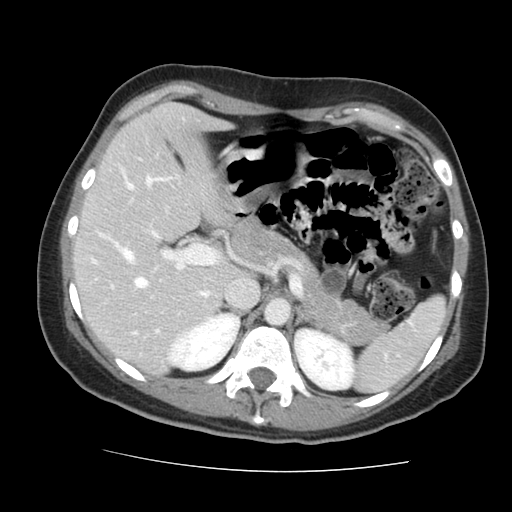
Contrast-enhanced abdominal CT, one axial slice. Position 94 of 144 along the scan axis. 120 kVp. Intravenous contrast given. Soft-tissue window (W 400 / L 40 HU). 512 × 512 image matrix. Female patient, age 46 years. From the clinical record (not read from this slice): diagnosis: colorectal cancer liver metastases, imaged before liver resection; multiple liver metastases: no; largest metastasis: 2.8 cm; disease in both lobes: no.
Structures marked on this image (expert manual segmentation):
- hepatic veins: bounding box [x1, y1, x2, y2] px = [122, 171, 207, 296]
- liver: [76, 105, 228, 372]
- planned liver remnant (the part of the liver to remain after resection): [76, 105, 228, 372]
- portal vein (with intrahepatic branches): [100, 230, 220, 332]